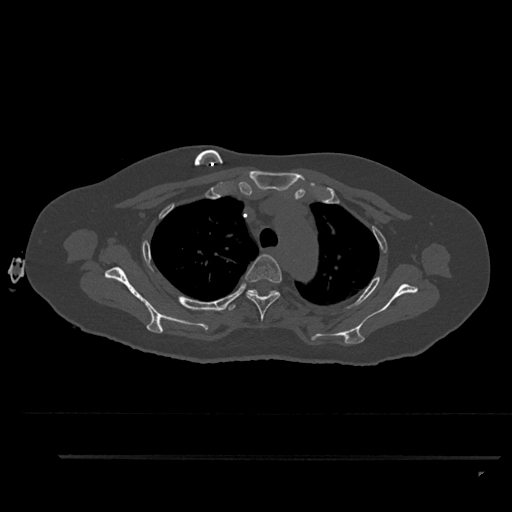
CT including the spine, one axial slice. Position 674 of 797 along the scan axis. 120 kVp. Bone window (W 1800 / L 400 HU). 512 × 512 image matrix, field of view 408 × 408 mm. Female patient, age 44 years. From the clinical record (not read from this slice): primary cancer: renal.
Outlined on this slice (semi-automatic segmentation, software-assisted and operator-edited):
- T3 vertebra: bounding box [x1, y1, x2, y2] px = [245, 254, 282, 321]
- T4 vertebra: [228, 289, 279, 311]